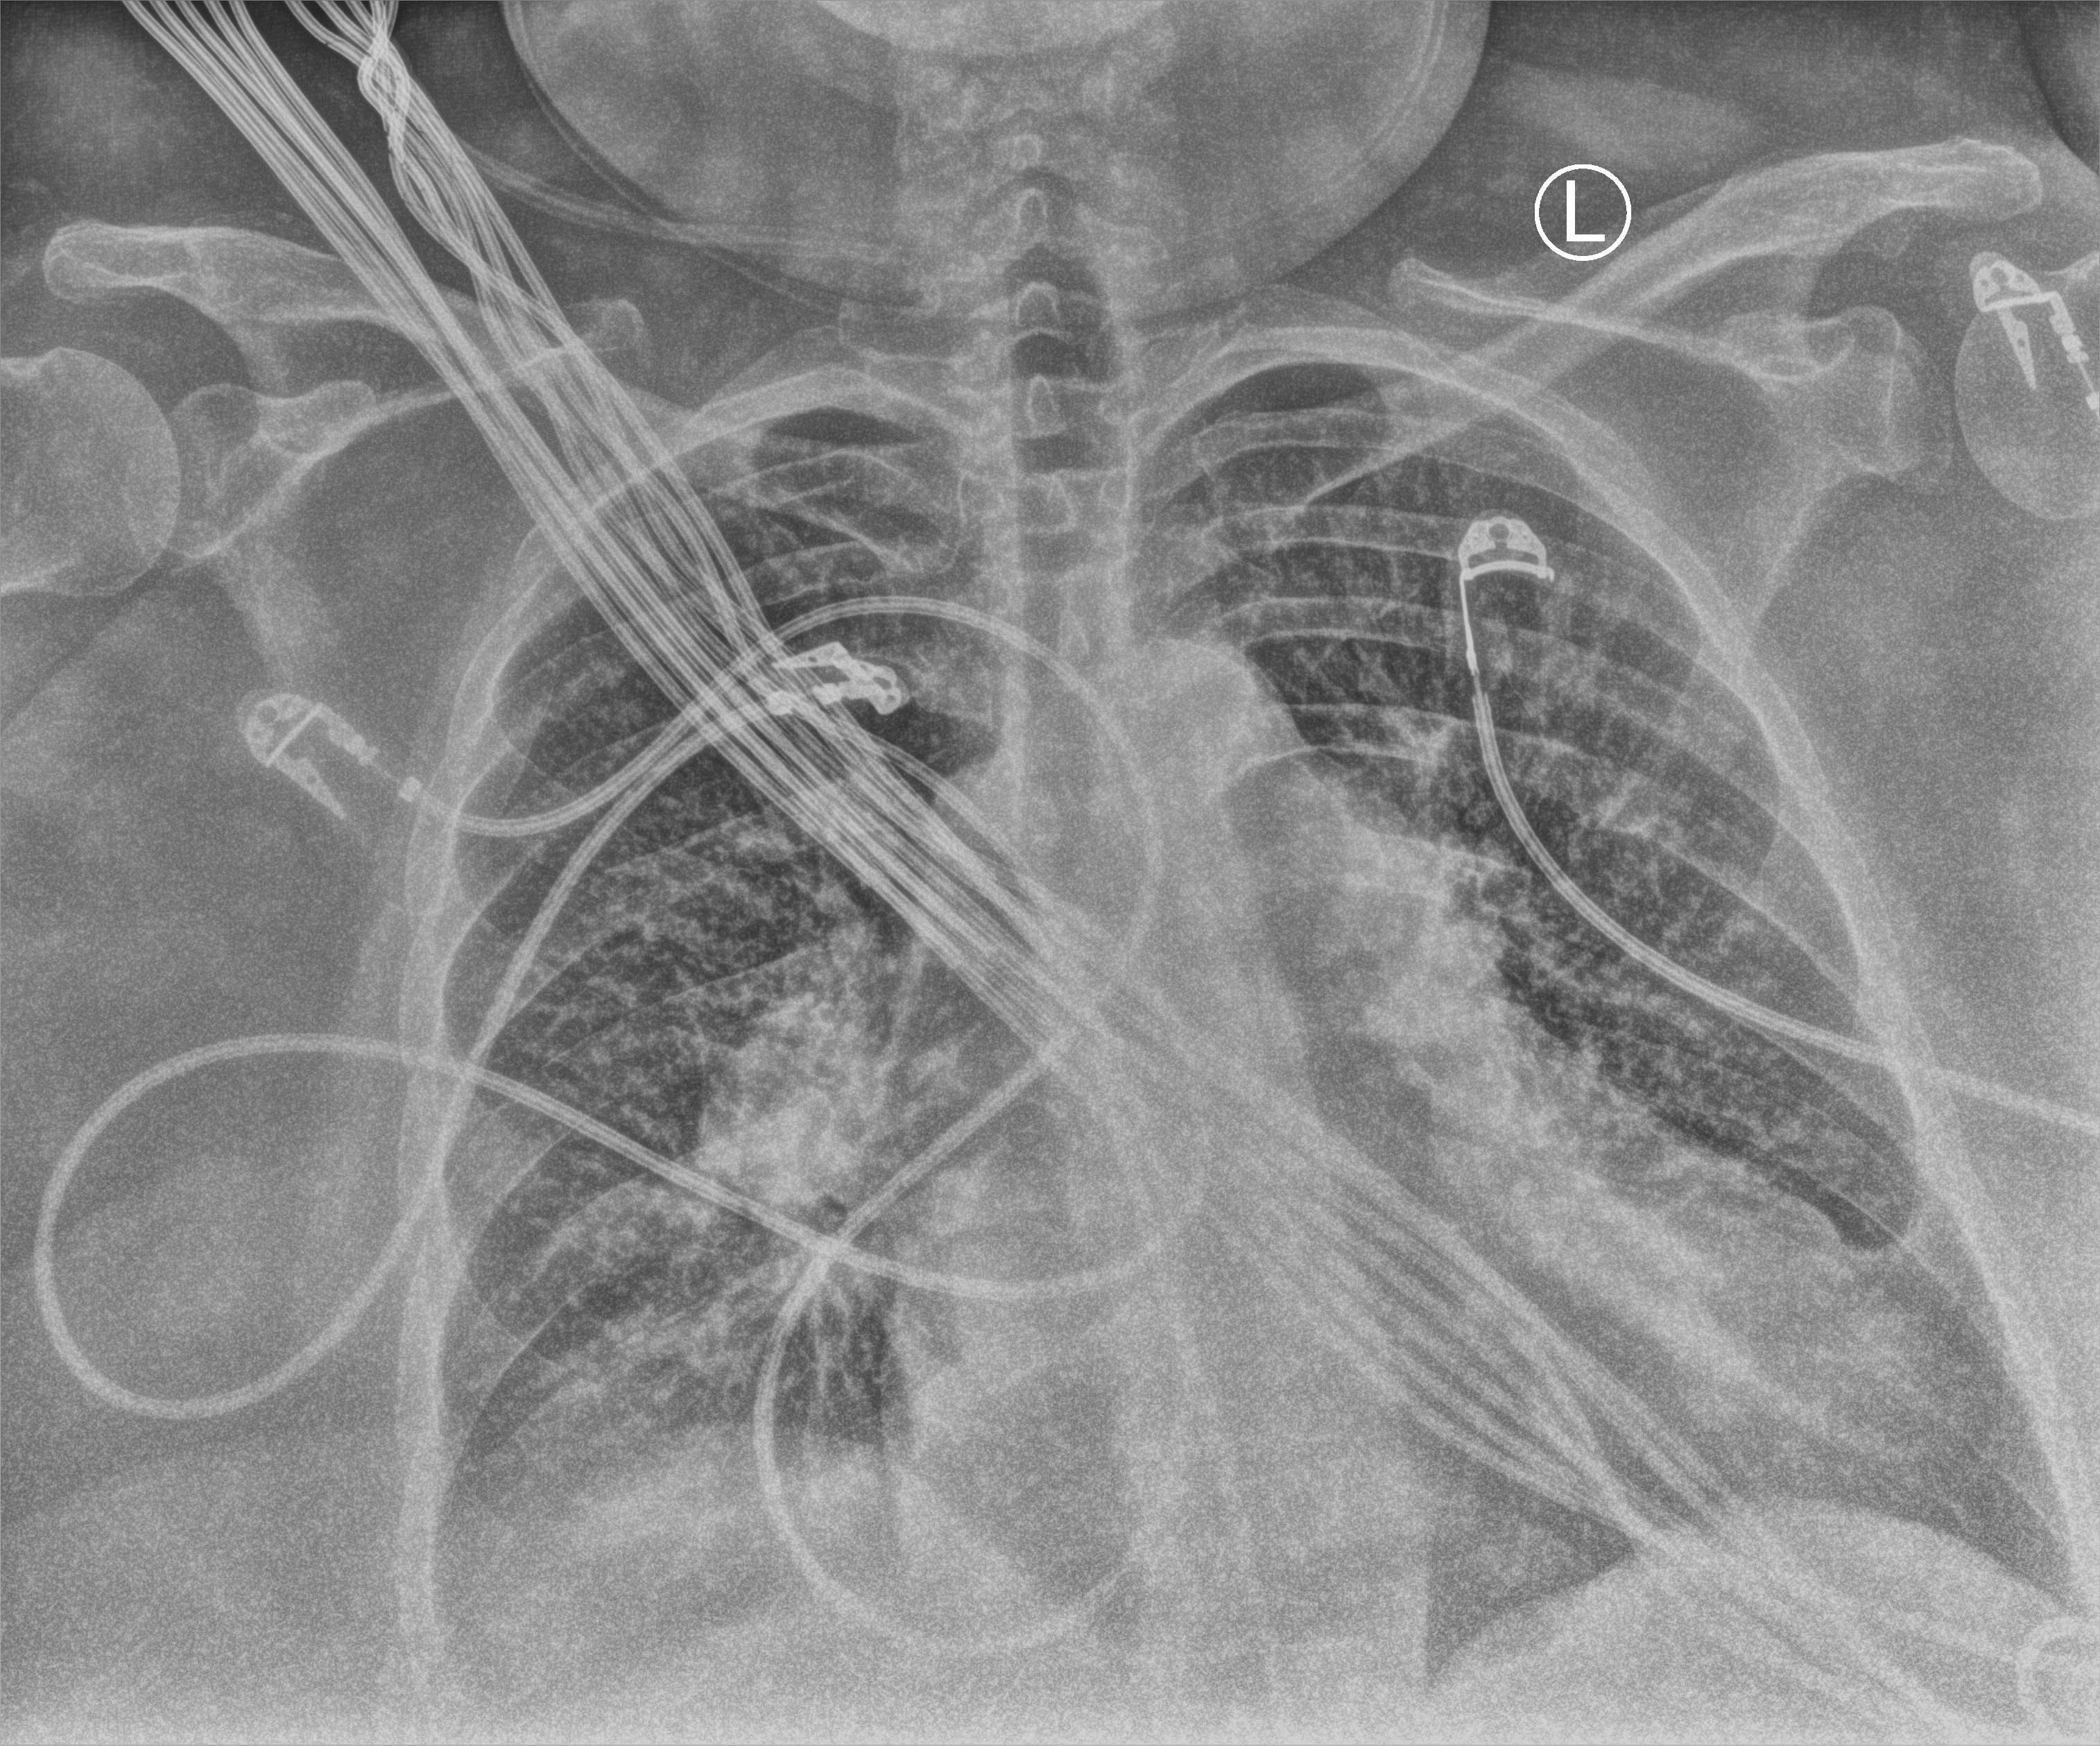
Bedside chest radiograph (computed radiography), anteroposterior (AP) projection. Female patient hospitalised with COVID-19, age 60–74 years.
Hospital-stay facts (about this admission, not read from this image; timing relative to this image not recorded): smoking status (admission record): former.